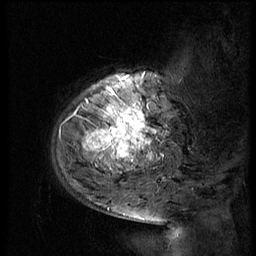
Breast MRI (dynamic contrast-enhanced), one sagittal slice. Slice 12 of 56 in the series (ordered by position). 3 images stored at this slice position (order not interpretable as contrast timing). 1.5 T. TE 4.2 ms, TR 9 ms. 2.5 mm slice thickness. 256 × 256 image matrix, field of view 180 × 180 mm. Female patient, age 51 years. Case-level facts recorded for this patient, not image findings: setting: breast cancer imaged before/during neoadjuvant chemotherapy; receptor status: triple-negative.
Structures marked on this image (semi-automatically segmented with operator editing):
- analysis volume of interest (the breast-tissue region the enhancement analysis was run in; not a lesion): bounding box <52,66,183,179> (left, top, right, bottom; pixels)
- tumour enhancement mask (voxels above the 140 % enhancement threshold inside the analysis volume of interest): <81,106,146,167>